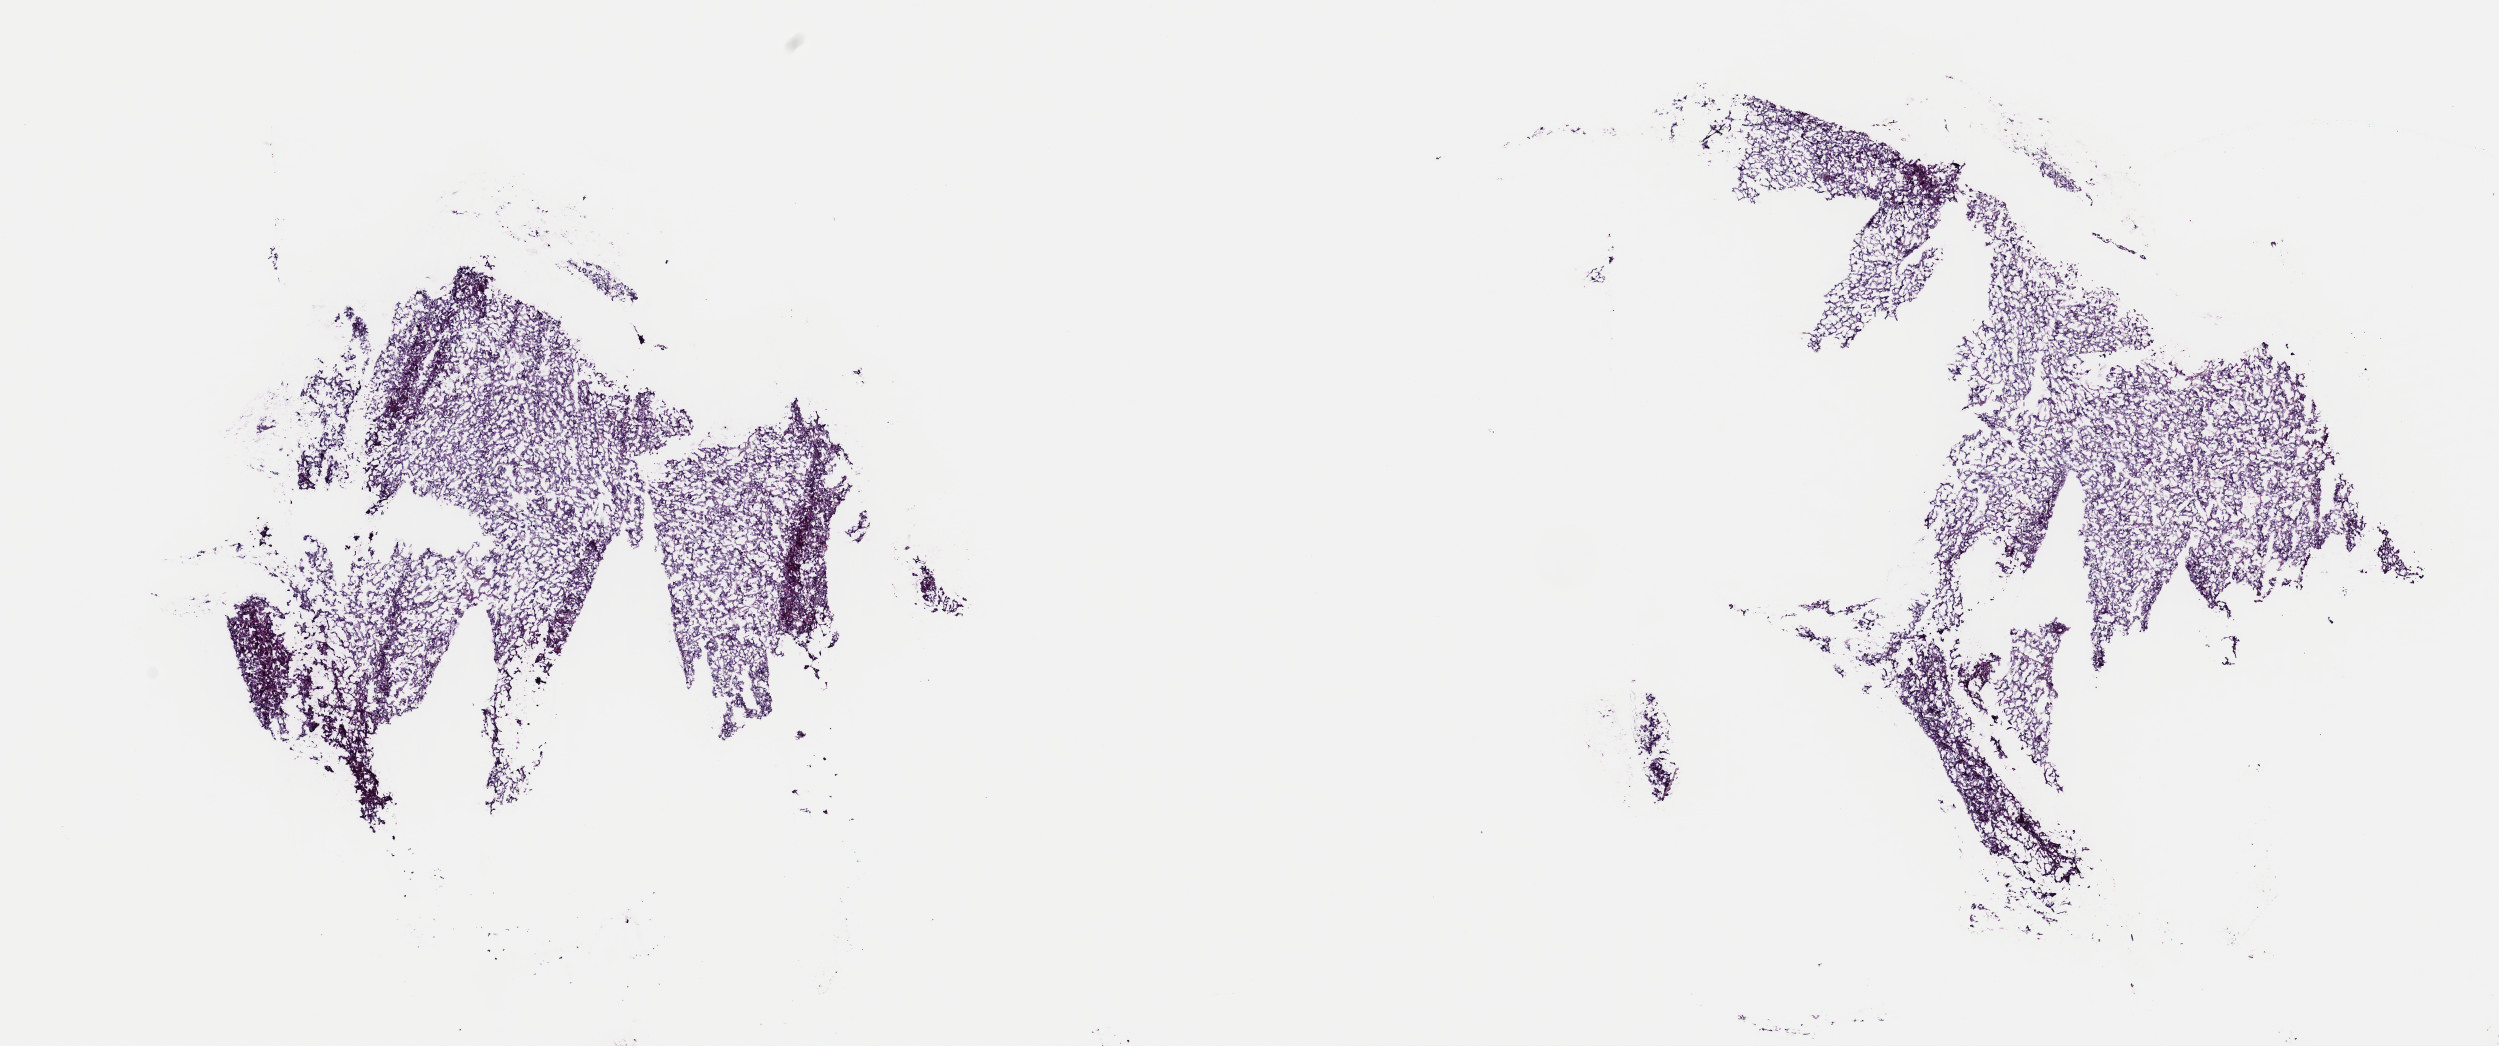
H&E-stained whole-slide image — shown as a low-resolution overview of the whole scanned area (about 19.7 x 8.3 mm, acquisition: 40x scan). Frozen section from the top of the tissue portion. Sample: primary tumour, adrenal gland. Male patient; age at initial diagnosis 43 years. Composition of this section per pathologist review: tumour cells 100%, tumour nuclei 80%, normal cells 0%, stromal cells 0%, necrosis 0%. Infiltration values recorded for this section: lymphocyte infiltration 1%, monocyte infiltration 0%, neutrophil infiltration 0%.
* histologic diagnosis: Pheochromocytoma, malignant